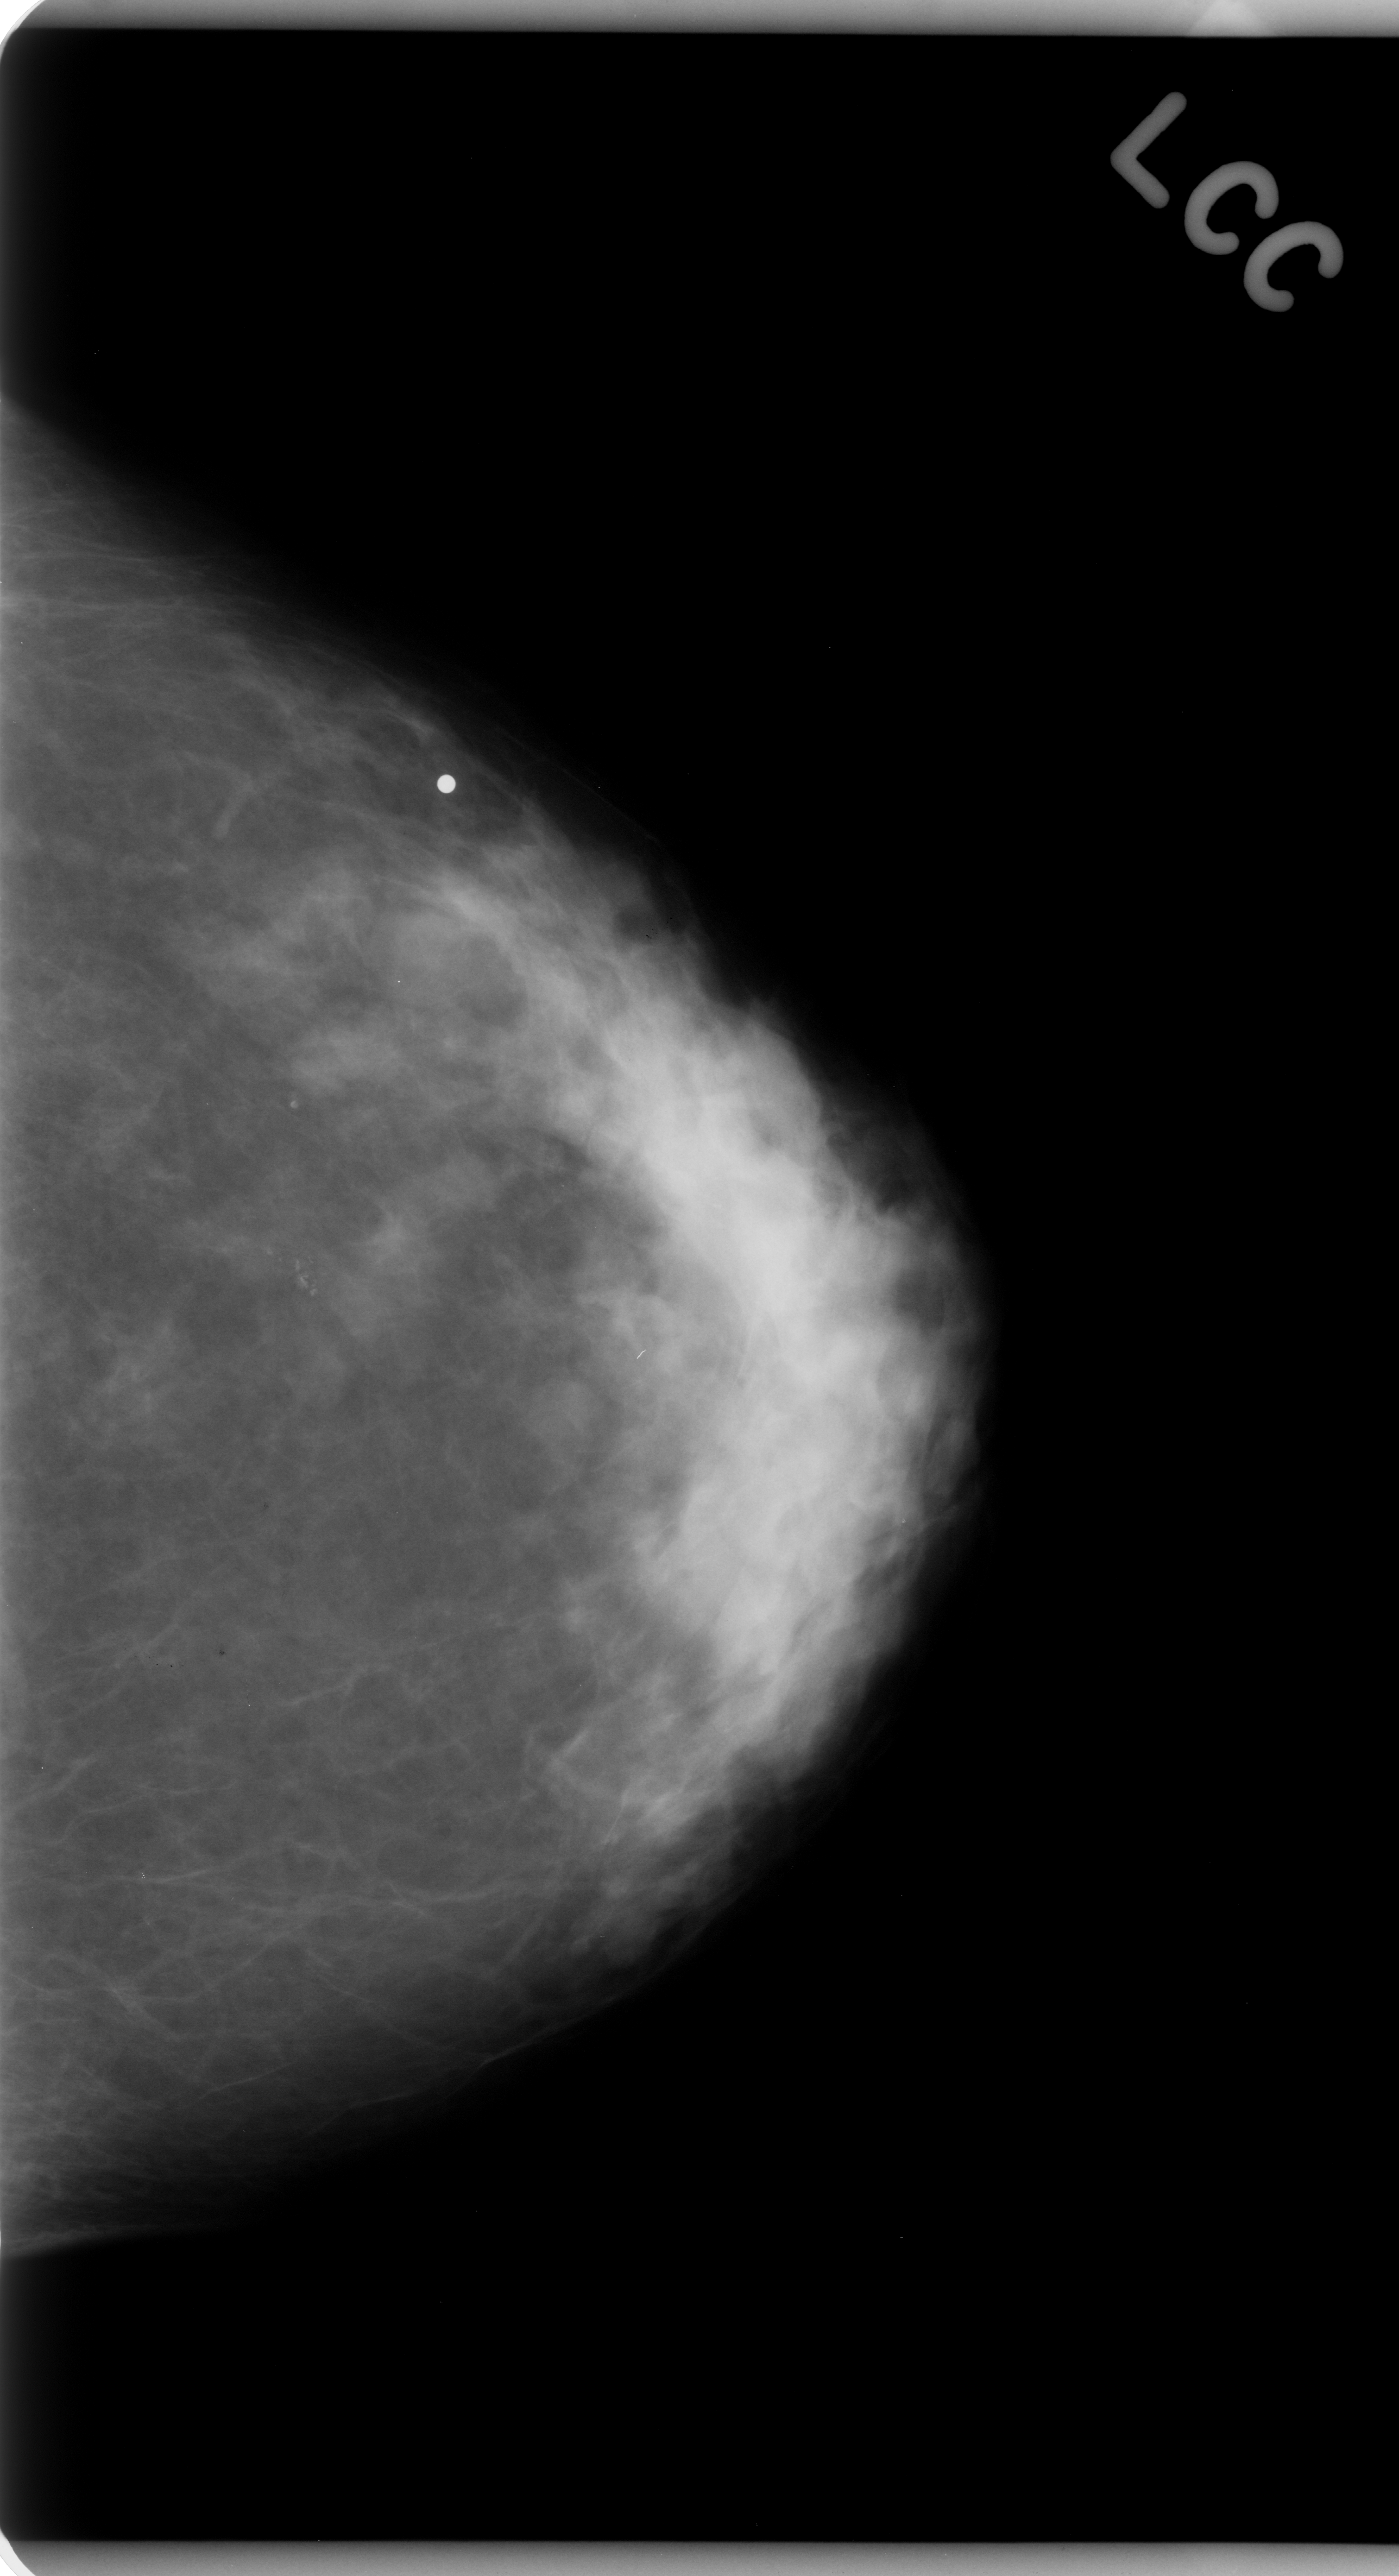
Scanned film-screen mammogram; left breast; craniocaudal (CC) view; BI-RADS breast density category 3 (scale 1–4); 1399 × 2576 image matrix.
Expert-marked regions of interest on this image (one box per marked abnormality):
- mass, shape round, margins circumscribed; BI-RADS assessment category 3; subtlety rating 4 on a 1 (subtle) to 5 (obvious) scale; pathology result (as recorded, not read from the image): benign: box from (x=376, y=845) to (x=498, y=946) px